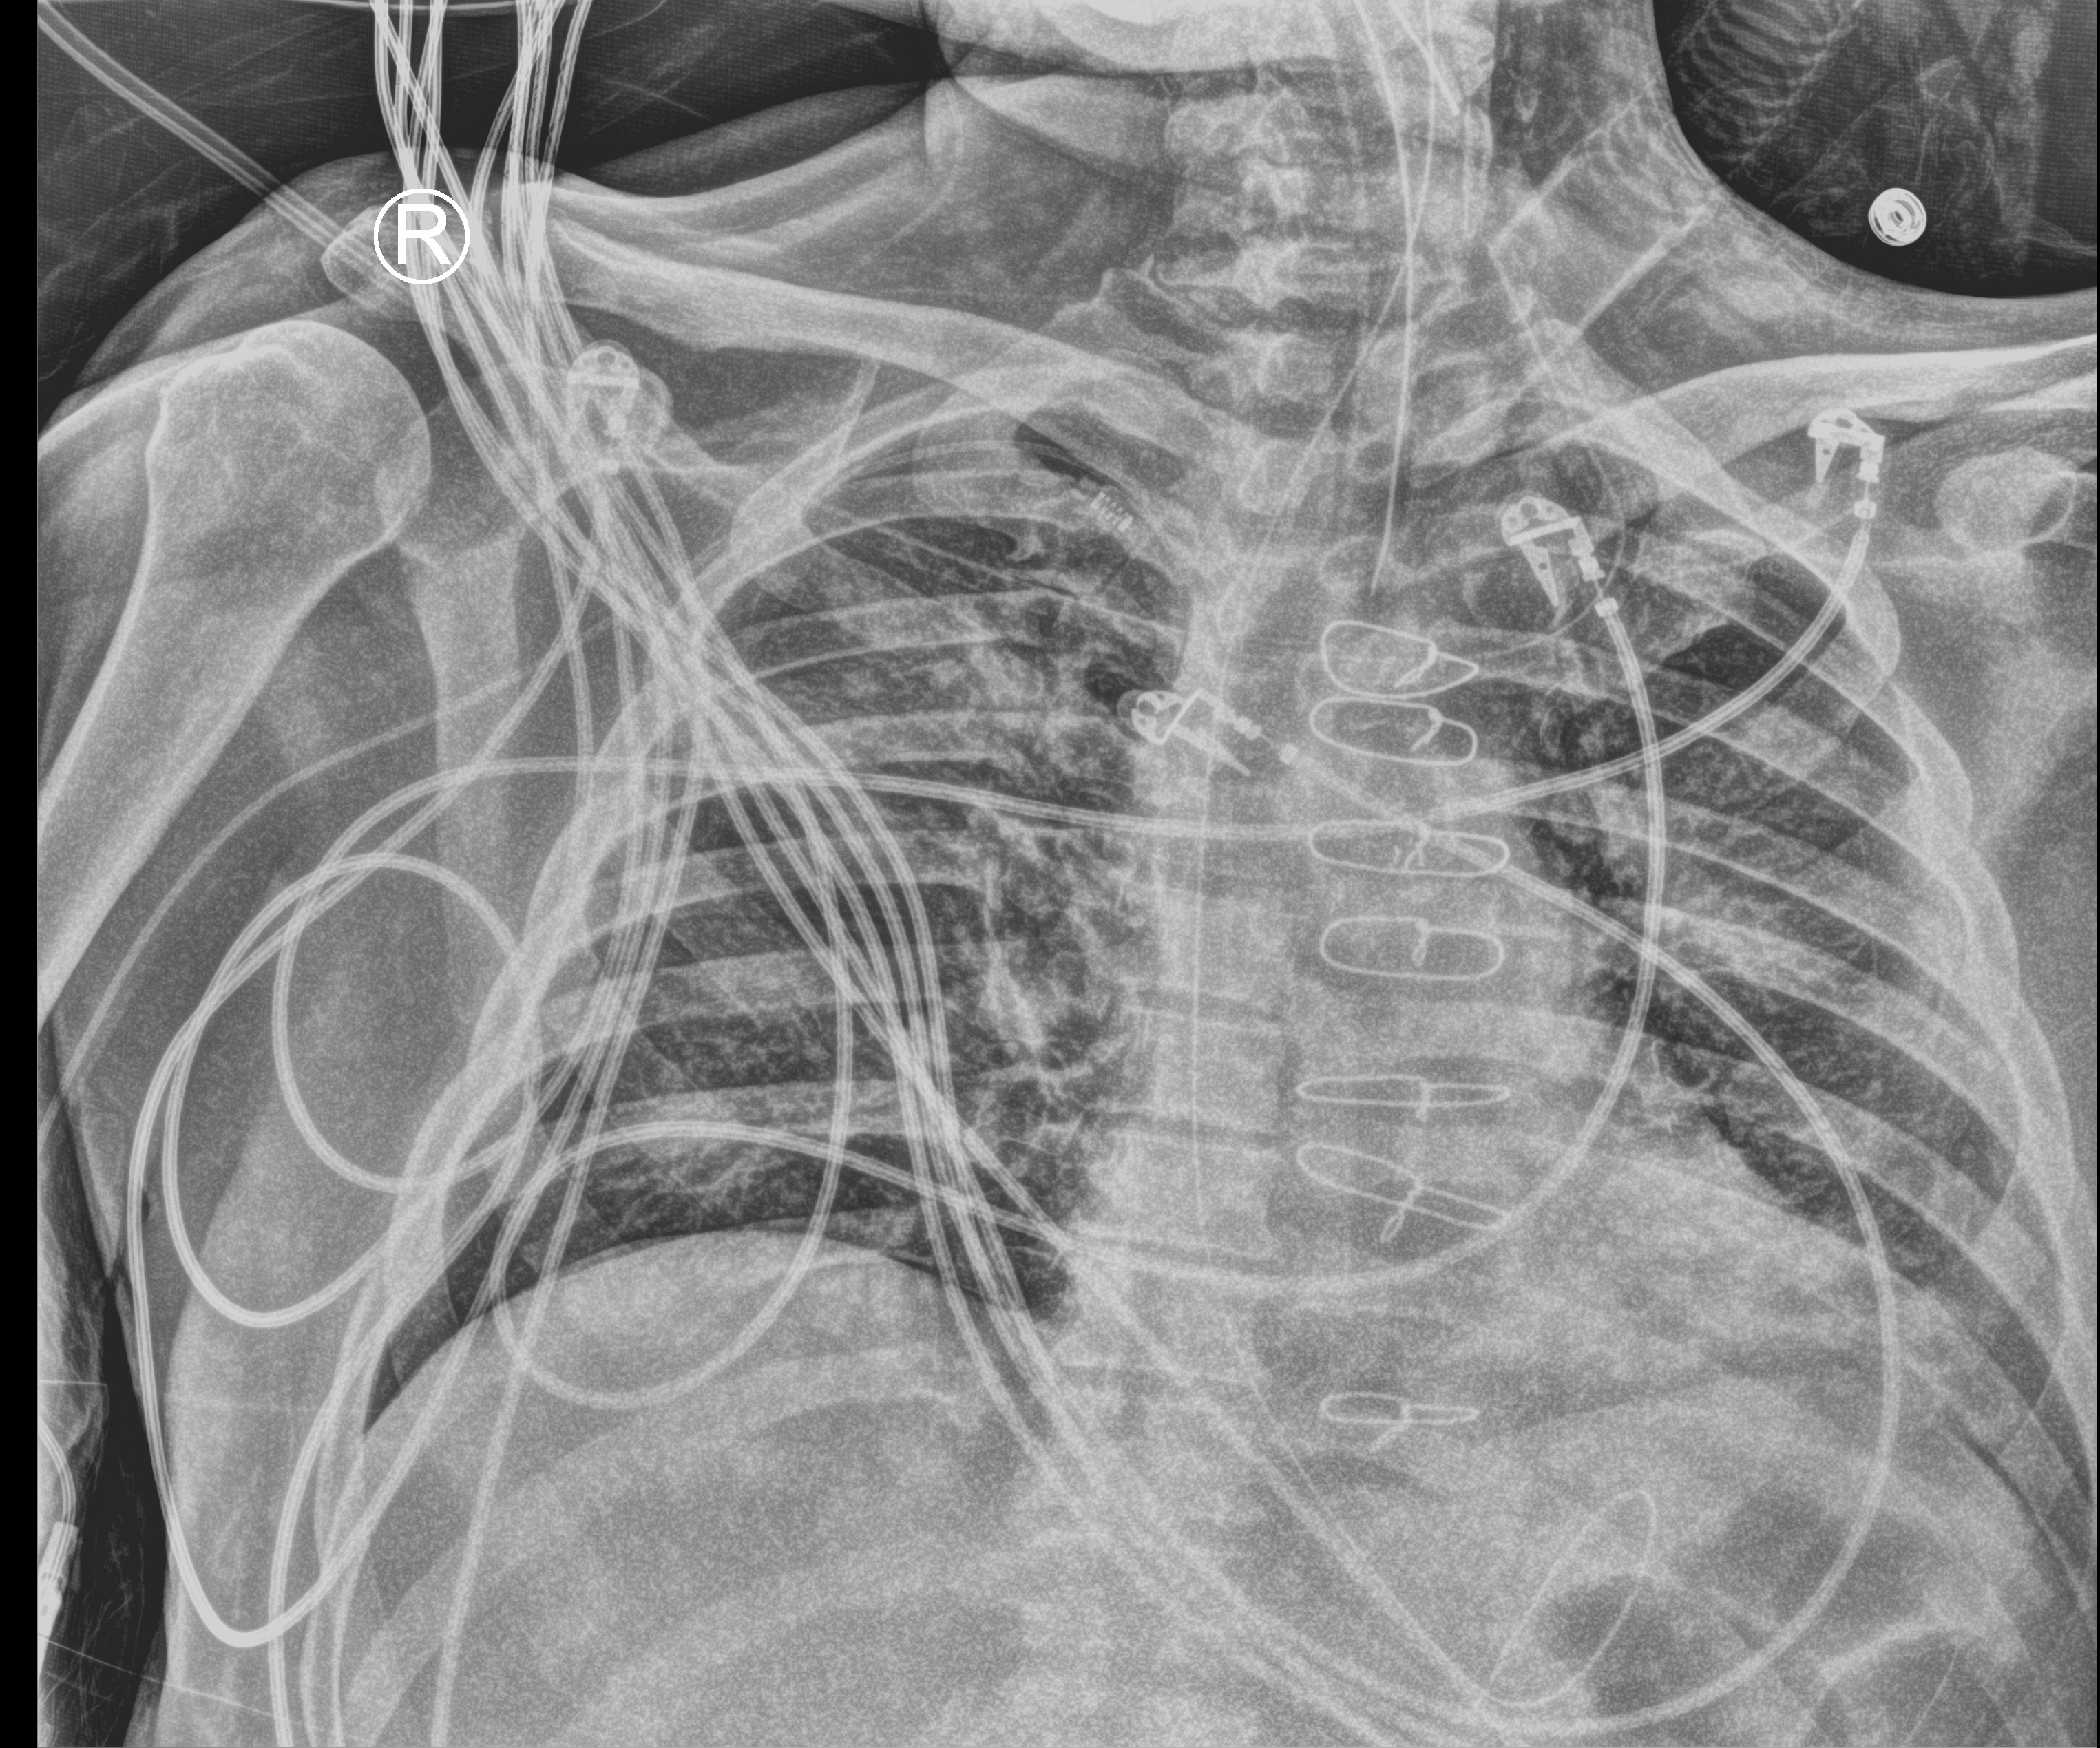
Bedside chest radiograph (computed radiography). Male patient hospitalised with COVID-19, age 60–74 years.
Hospital-stay facts (about this admission, not read from this image; timing relative to this image not recorded): mechanically ventilated during this hospital stay: yes; admitted to intensive care during this hospital stay: yes.